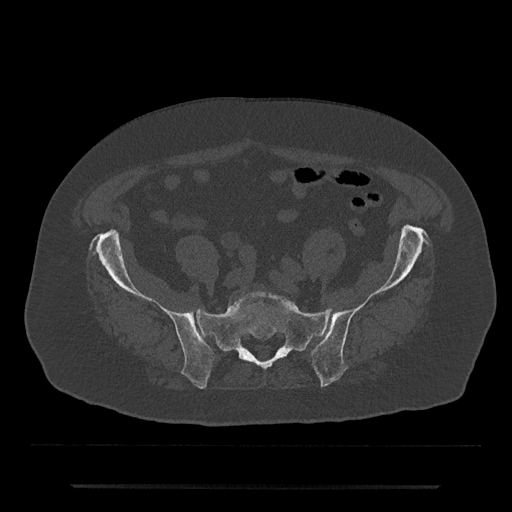
CT including the spine, one axial slice; slice 234 of 797 in the series (ordered by position); reconstruction kernel Br40s/3; 120 kVp; bone window (W 1800 / L 400 HU); 0.5 mm slice thickness; 512 × 512 image matrix, field of view 434 × 434 mm. Male patient, age 80 years. Case-level facts recorded for this patient, not image findings: primary cancer: prostate; vertebrae with lytic lesions (as recorded): L1, T11.
Structures marked on this image (semi-automatic segmentation, software-assisted and operator-edited):
- L5 vertebra: bounding box (x1, y1, x2, y2) in pixels: (235, 291, 288, 304)